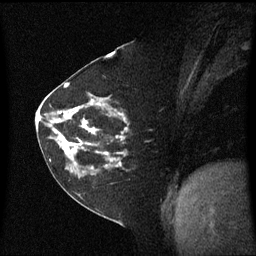
Breast MRI (dynamic contrast-enhanced), one sagittal slice. Dynamic contrast-enhanced series, image 2 of 3 at this slice position (ordered by acquisition). 1.5 T. TE 4.2 ms, TR 8.4 ms. 2 mm slice thickness. 256 × 256 image matrix, field of view 210 × 210 mm. Patient: female, 60 years. Case-level facts recorded for this patient, not image findings: setting: breast cancer imaged before/during neoadjuvant chemotherapy; receptor status: triple-negative.
Annotated regions visible in this slice (semi-automatically segmented with operator editing):
- analysis volume of interest (the breast-tissue region the enhancement analysis was run in; not a lesion): box from (x=45, y=99) to (x=131, y=182) px
- tumour enhancement mask (voxels above the 70 % enhancement threshold inside the analysis volume of interest): (x=54, y=101)–(x=123, y=166)